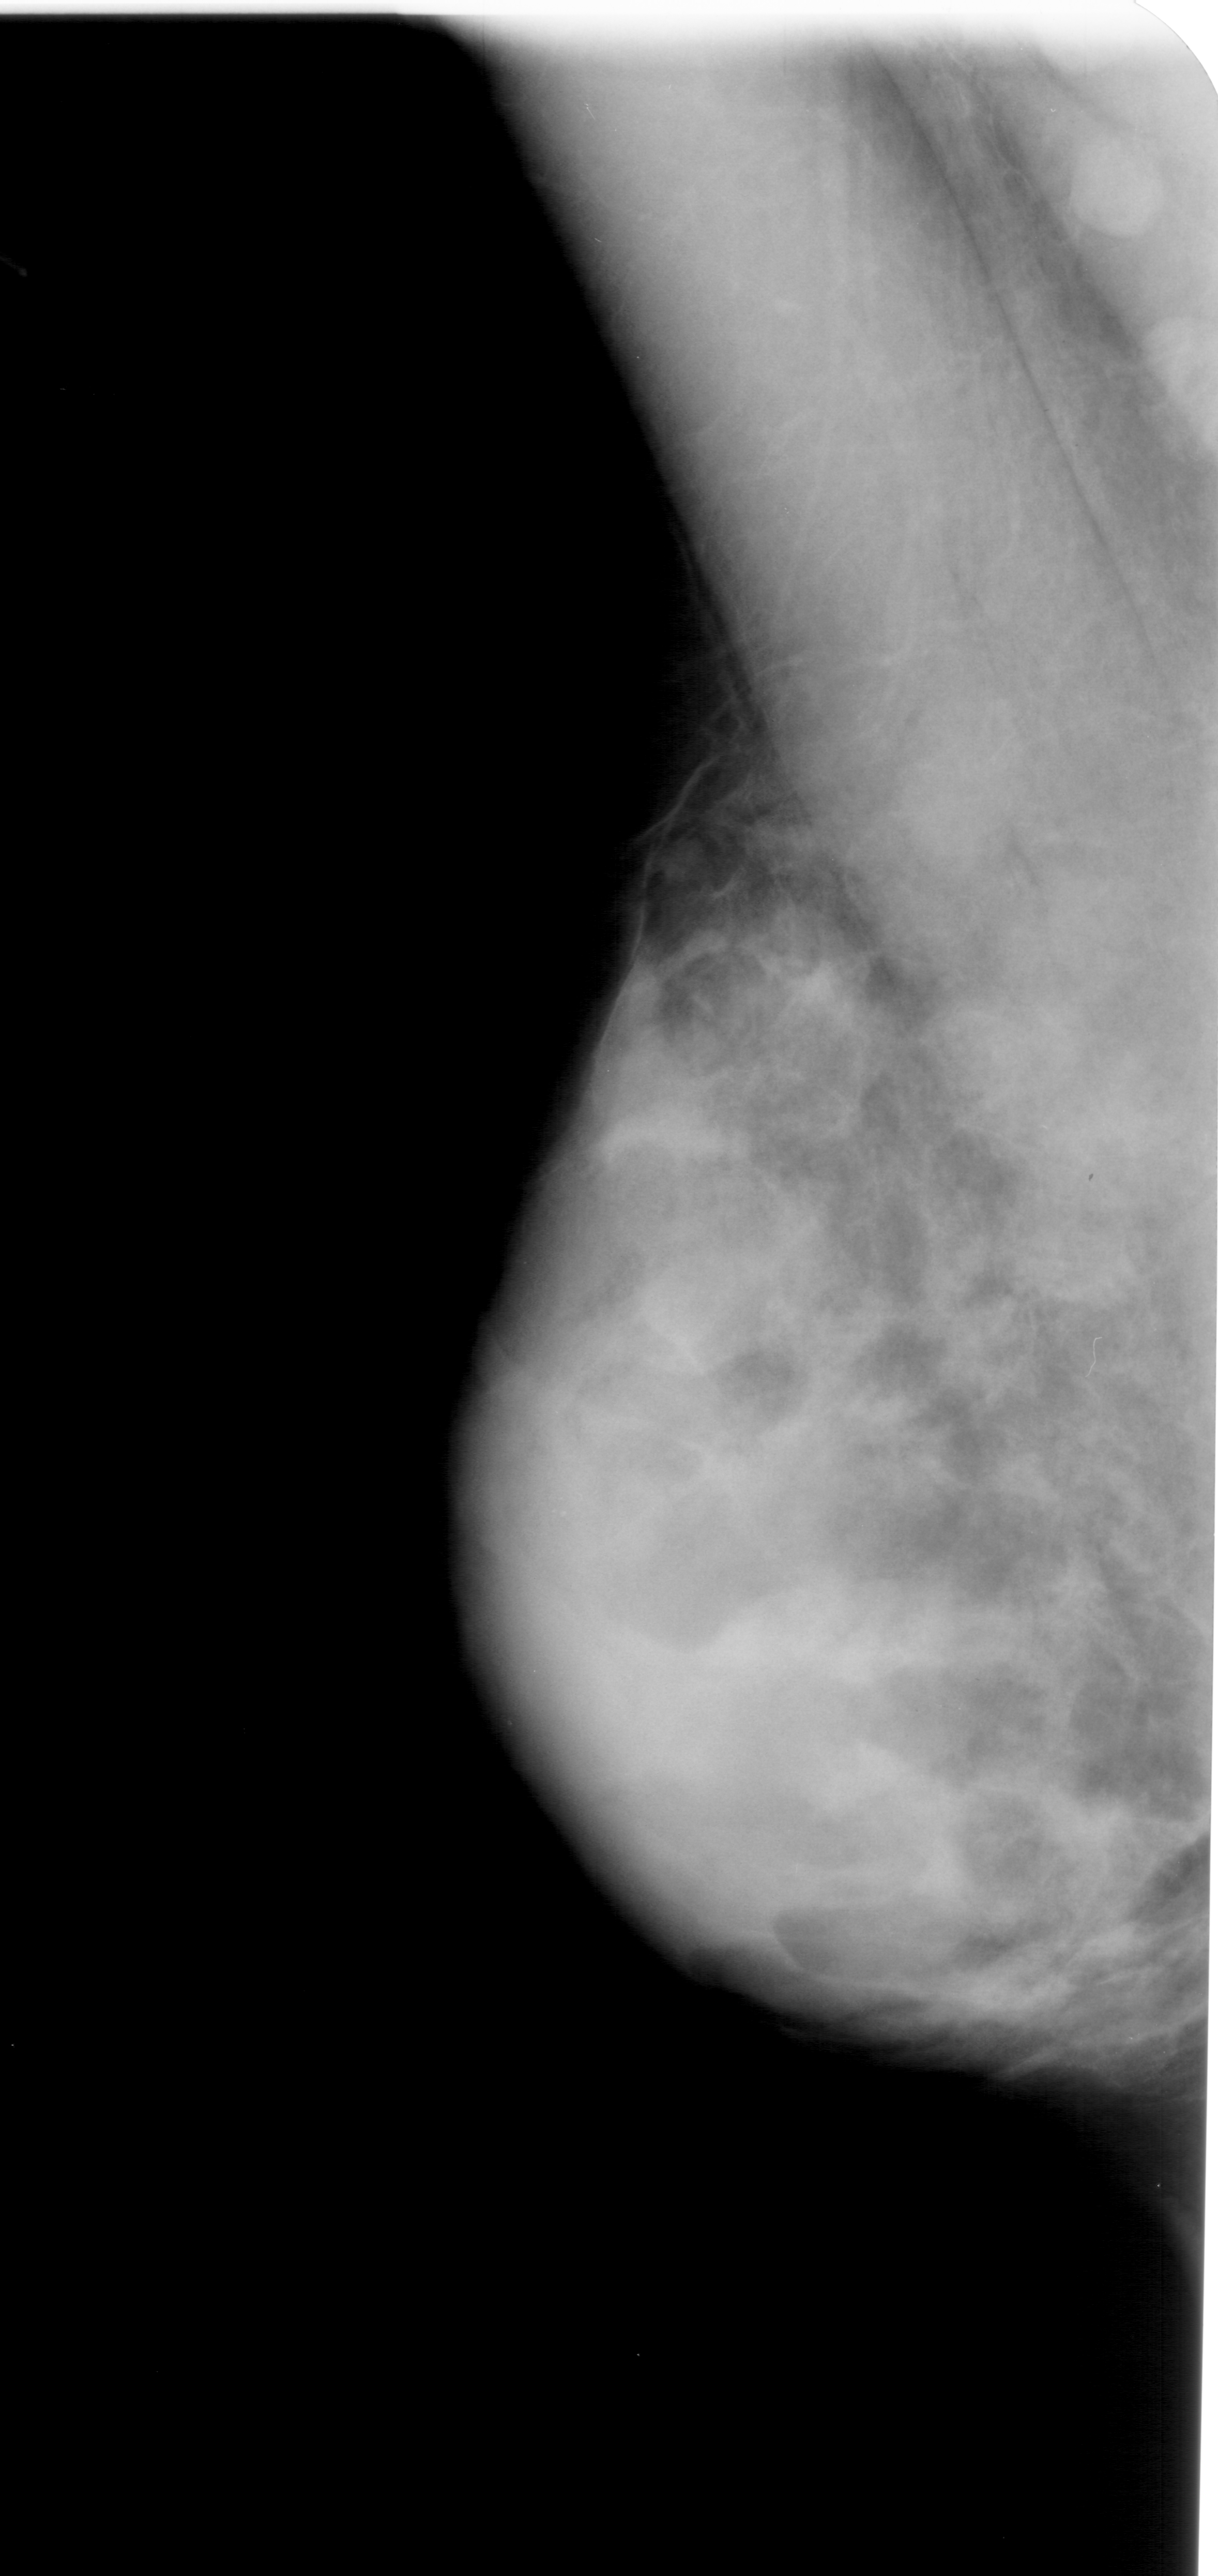
Digitized screen-film mammogram, left breast, MLO view, breast composition: extremely dense (BI-RADS density category 4 of 4).
Calcifications, morphology pleomorphic, distribution clustered; BI-RADS assessment category 4; pathology (as recorded): benign.